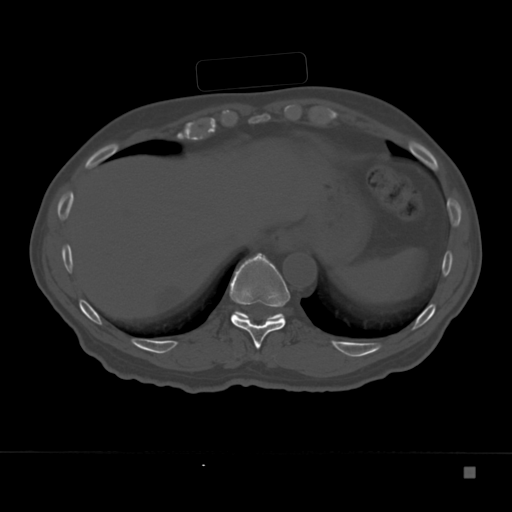
CT including the spine, one axial slice; slice 168 of 332 in the series (ordered by position); 120 kVp; bone window (W 1800 / L 400 HU); 1.5 mm slice thickness; 512 × 512 image matrix, field of view 389 × 389 mm. Patient: male, 72 years. Case-level facts recorded for this patient, not image findings: primary cancer: skeletal.
Outlined on this slice (semi-automatically segmented with operator editing):
- T10 vertebra: box from (x=230, y=253) to (x=290, y=349) px
- T11 vertebra: (x=234, y=311)–(x=284, y=320)